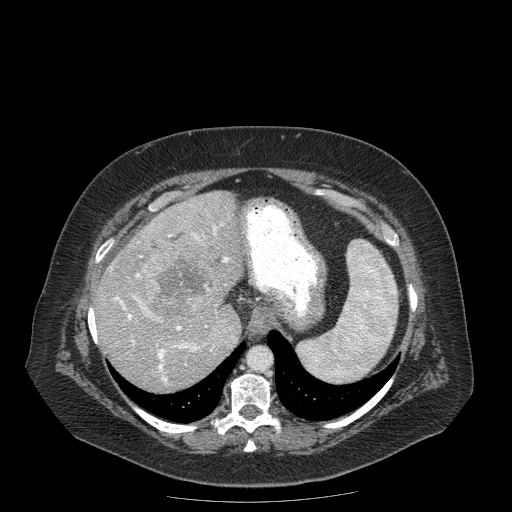
Contrast-enhanced abdominal CT (liver protocol), one axial slice. Slice 137 of 204 in the series (ordered by position). Reconstruction kernel STANDARD. 120 kVp. Soft-tissue window (W 400 / L 40 HU). 2.5 mm slice thickness. 512 × 512 image matrix, field of view 440 × 440 mm. Case-level facts recorded for this patient, not image findings: diagnosis: hepatocellular carcinoma (patient treated with transarterial chemoembolisation; whether this scan precedes or follows treatment is not stated here); TNM stage (as recorded): Stage-IIIB; Child-Pugh class: A; tumour differentiation: well differentiated.
Annotated regions visible in this slice (semi-automatically segmented with operator editing):
- liver parenchyma outside the tumour (the mass and vessels are separate outlines, so this box may not span the whole liver): bounding box (x1, y1, x2, y2) in pixels: (94, 190, 244, 390)
- mass: (140, 238, 228, 318)
- liver vessels: (110, 224, 229, 384)